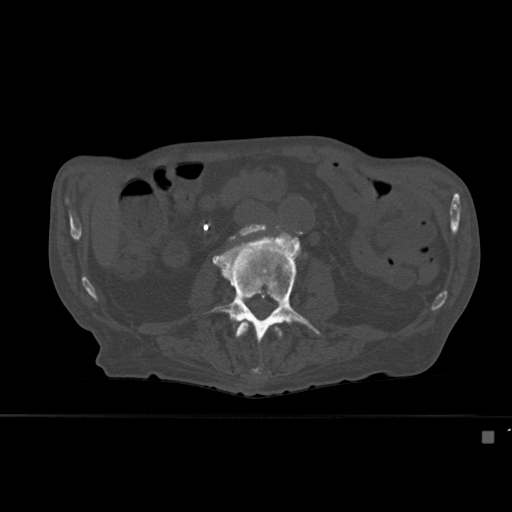
CT including the spine, one axial slice; slice 214 of 527 in the series (ordered by position); bone window (W 1800 / L 400 HU); 1.5 mm slice thickness; 512 × 512 image matrix. Patient: male, 78 years. Case-level facts recorded for this patient, not image findings: primary cancer: prostate.
Annotated regions visible in this slice (semi-automatic segmentation, software-assisted and operator-edited):
- L2 vertebra: bounding box [x1, y1, x2, y2] px = [235, 320, 282, 380]
- L3 vertebra: [205, 227, 322, 374]
- L4 vertebra: [231, 227, 267, 238]